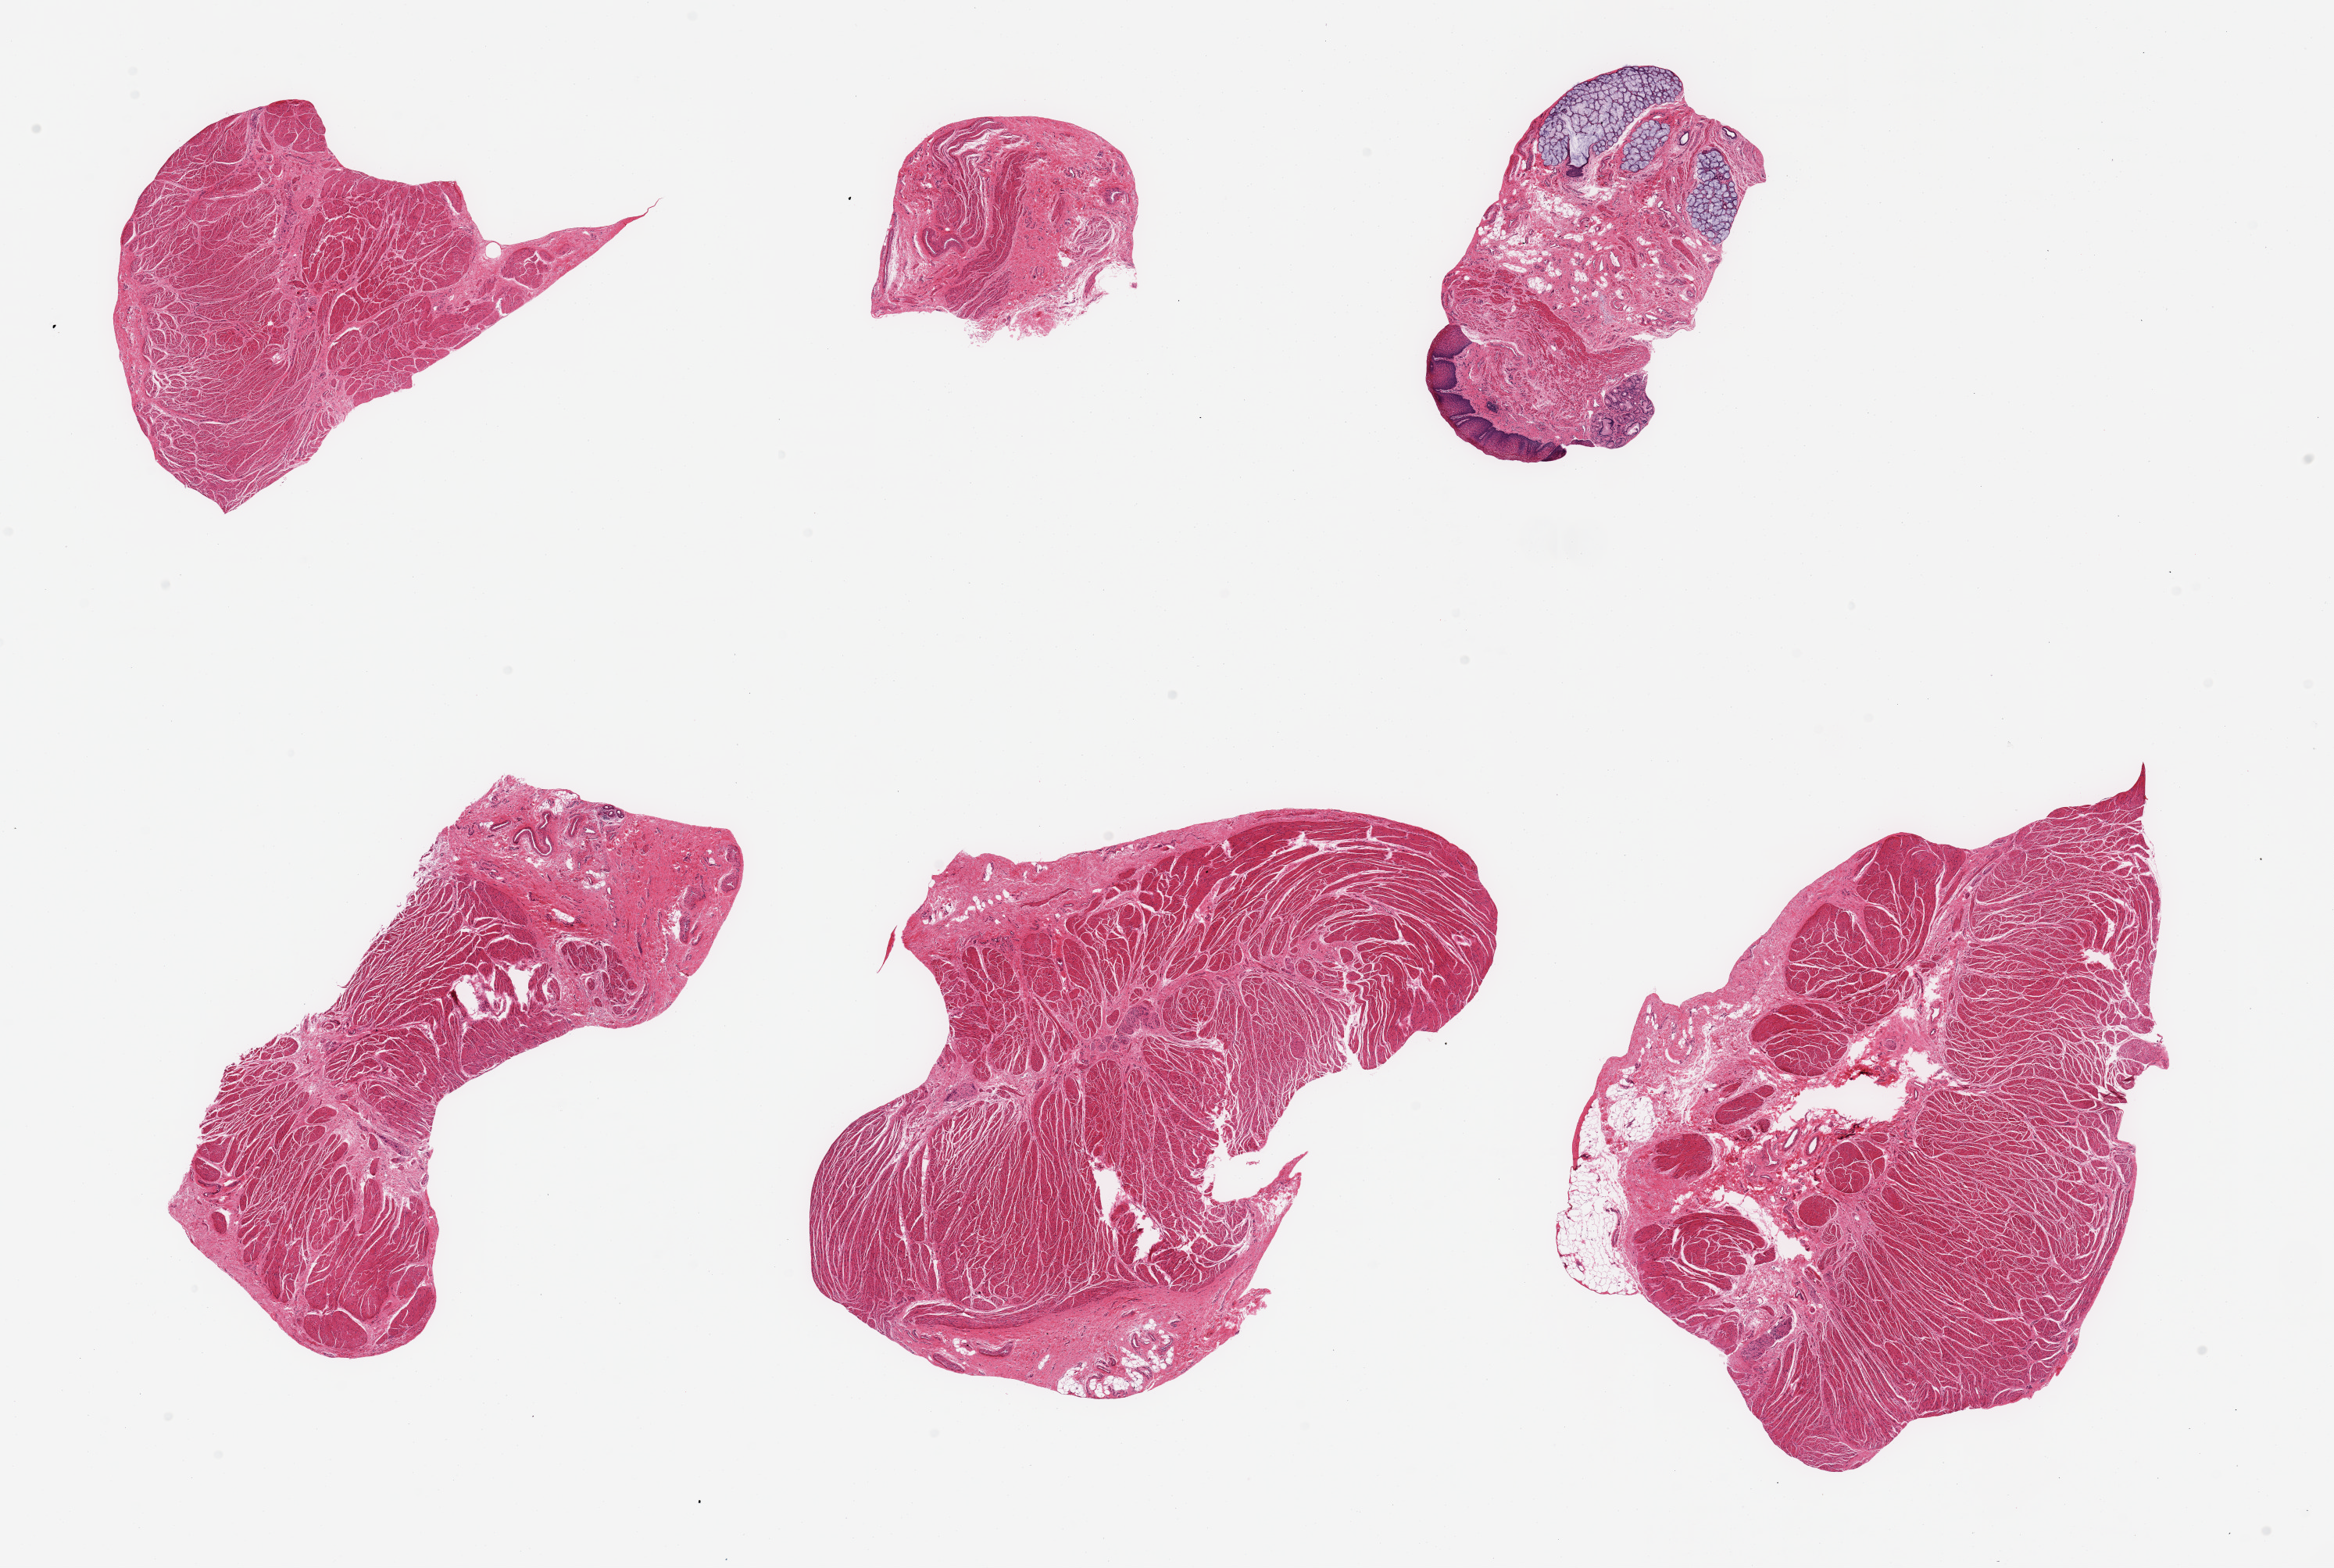
Haematoxylin and eosin whole-slide image — a low-resolution overview of the entire scanned area, about 23.6 x 15.9 mm; PAXgene-fixed paraffin-embedded (PFPE) section; target tissue: gastroesophageal junction; donor tissue sample. Donor sex: female.
Pathologist's review note for this sample: 6 pieces, target muscularis; Trace glandular elements/squamous mucosa.